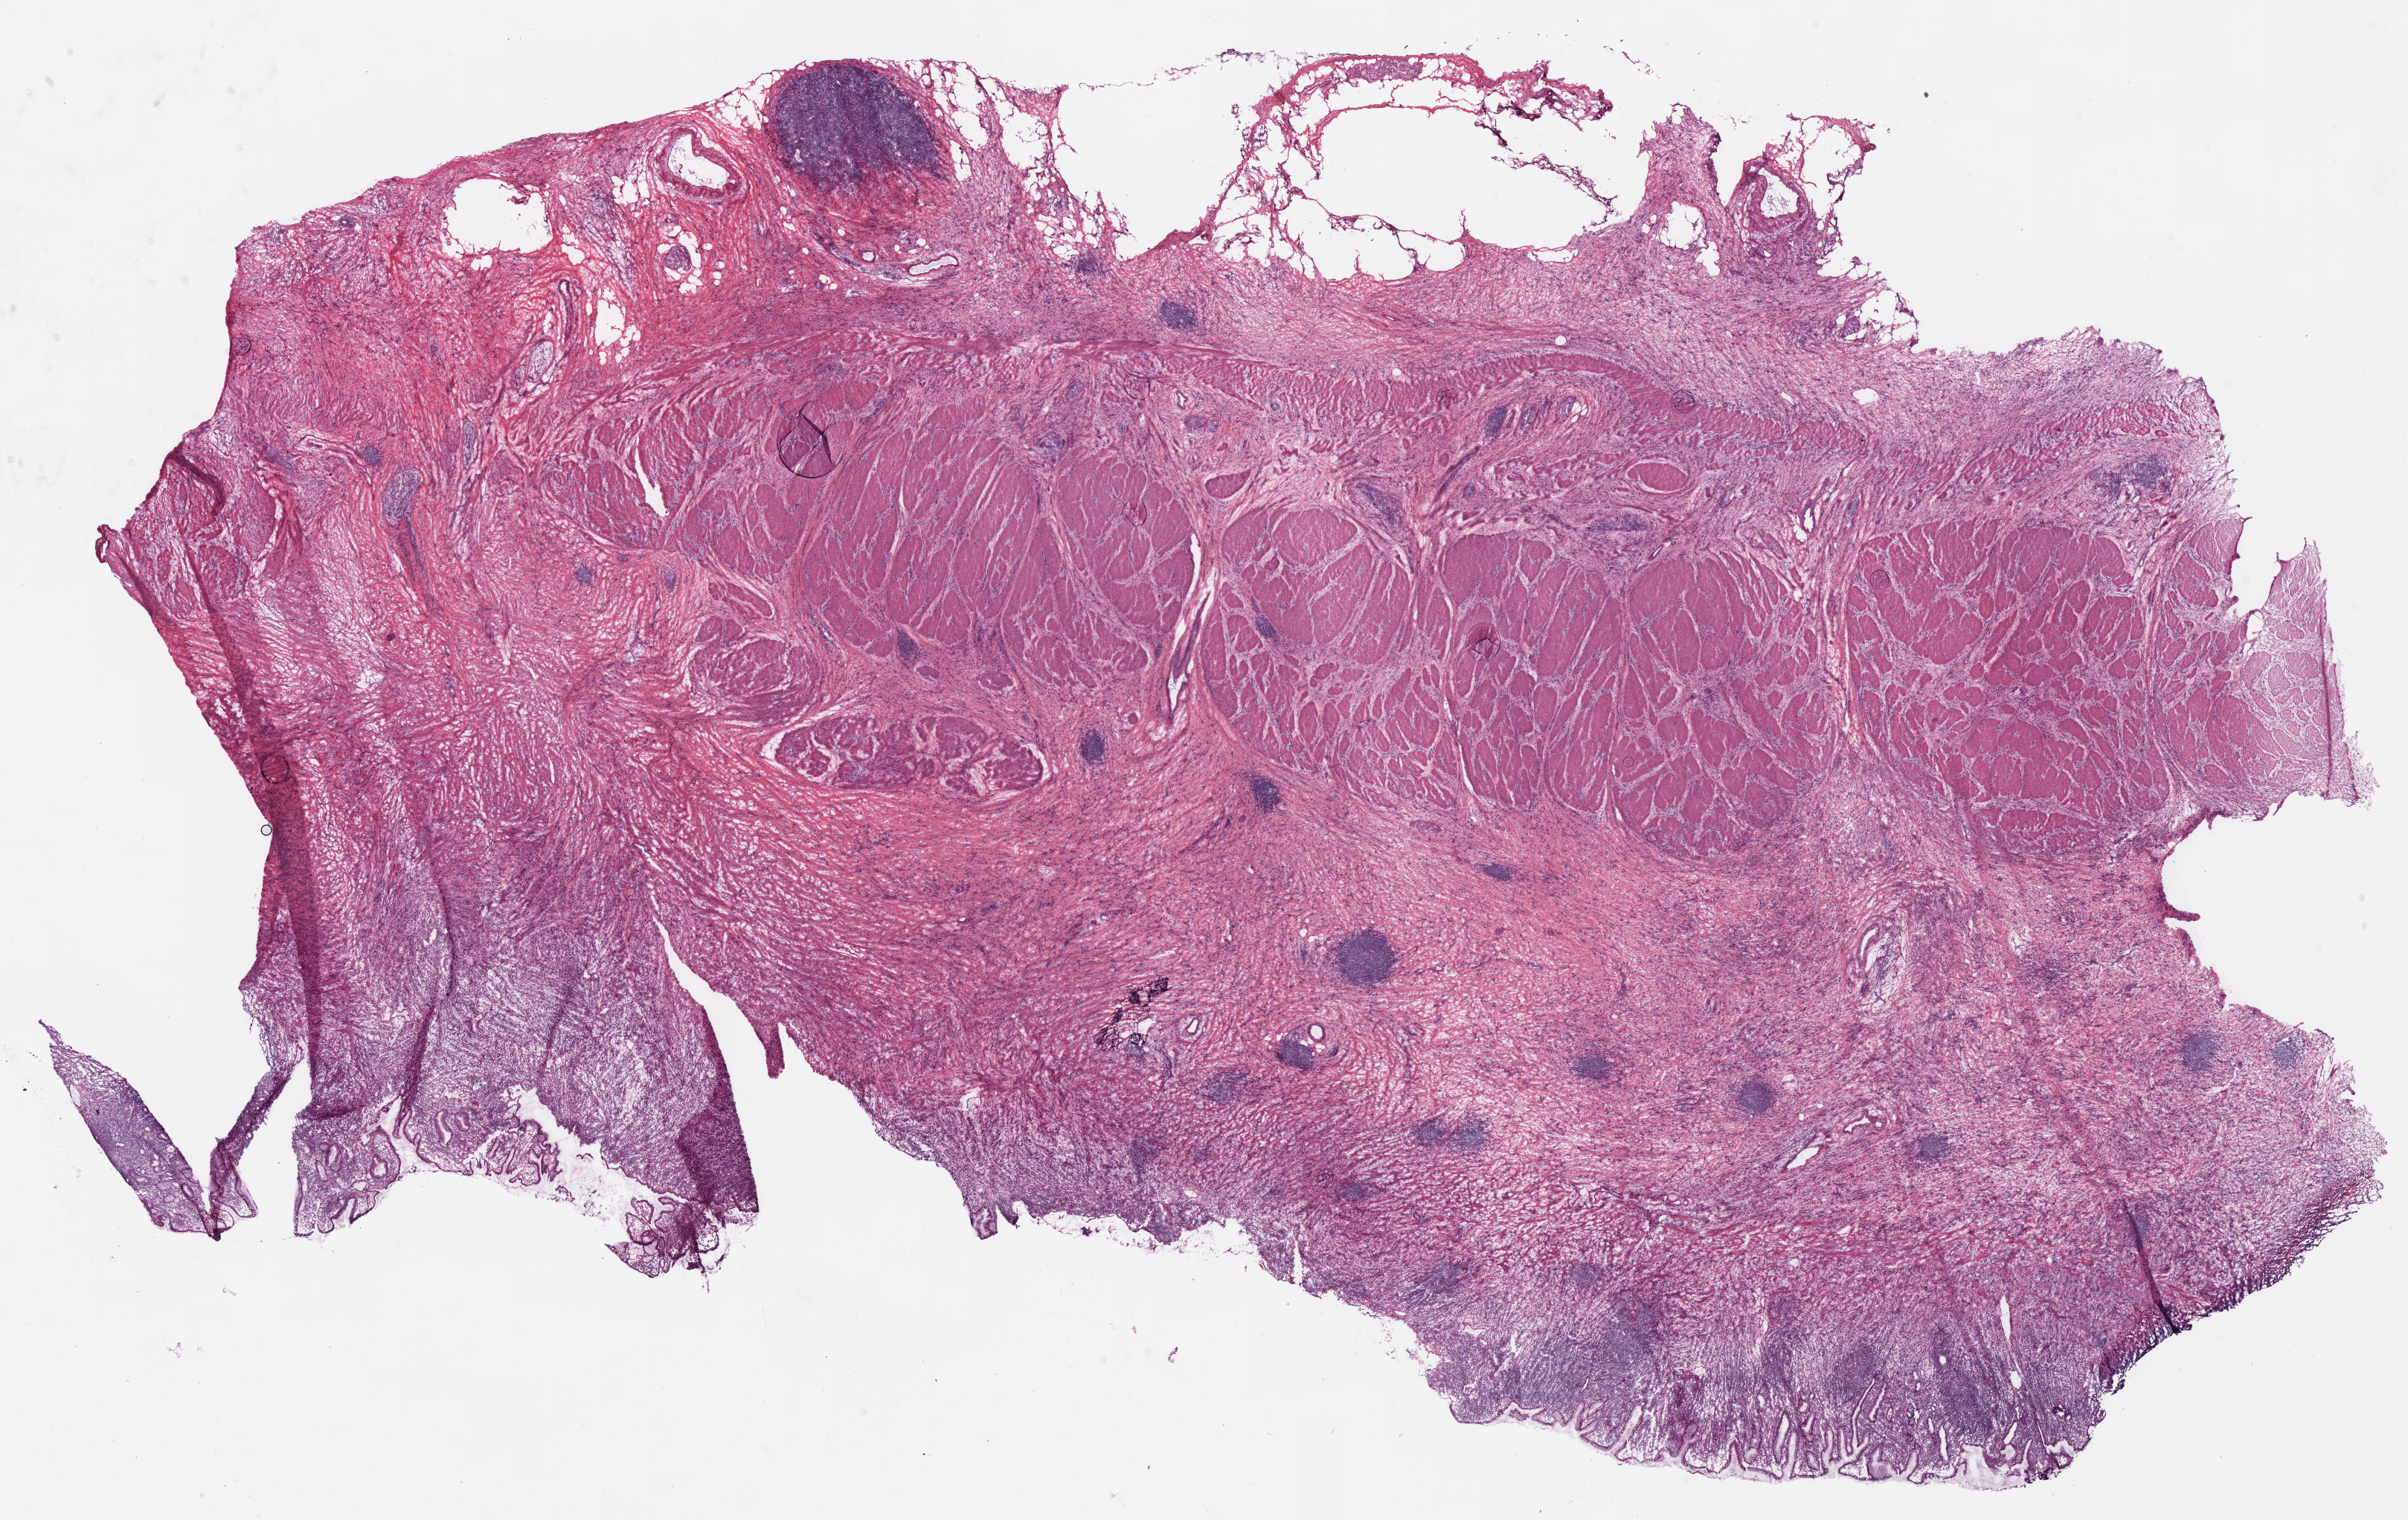
Whole-slide histology image, Hematoxylin and eosin (H&E) stained, low-resolution overview of the scanned area, about 25.5 x 16.1 mm; frozen section from the bottom of the tissue portion; primary tumour sample from the stomach. Female patient; age at initial diagnosis 63 years. Histologic grade: G3 (poorly differentiated). Composition of this section per pathologist review: tumour cells 55%, tumour nuclei 60%, normal cells 5%, stromal cells 40%, necrosis 0%.
Lymph nodes positive (case pathology): 1 of 3 examined. AJCC pathologic stage: IIIB (7th edition). Diagnosis: Carcinoma, diffuse type (fundus of stomach).